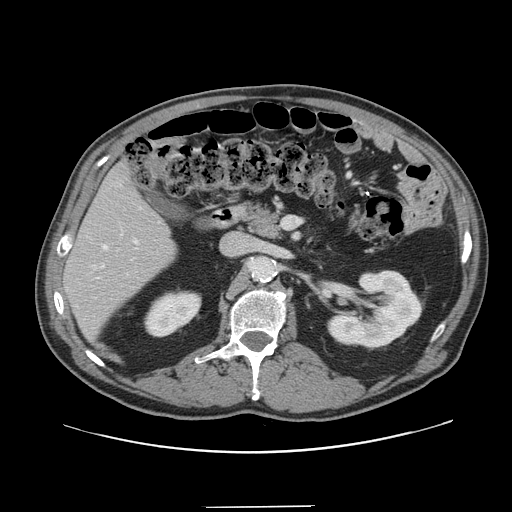
Contrast-enhanced abdominal CT, one axial slice. Slice 71 of 139 in the series (ordered by position). Intravenous contrast given. Soft-tissue window (W 400 / L 40 HU). 2.5 mm slice thickness. 512 × 512 image matrix, field of view 397 × 397 mm. Male patient, age 64 years. From the clinical record (not read from this slice): diagnosis: colorectal cancer liver metastases, imaged before liver resection; multiple liver metastases: yes; largest metastasis: 3.5 cm; chemotherapy before resection: yes.
Outlined on this slice (expert manual segmentation):
- hepatic veins: bounding box (x1, y1, x2, y2) in pixels: (101, 245, 108, 268)
- liver: (65, 166, 176, 338)
- planned liver remnant (the part of the liver to remain after resection): (65, 166, 176, 337)
- portal vein (with intrahepatic branches): (97, 239, 138, 279)